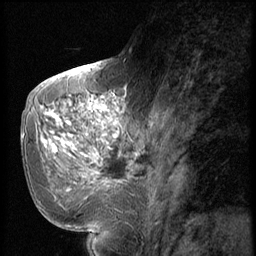
Breast MRI (dynamic contrast-enhanced), one sagittal slice. Slice 26 of 56 in the series (ordered by position). Dynamic contrast-enhanced series, image 2 of 2 at this slice position (ordered by acquisition). 1.5 T. TE 4.2 ms, TR 9 ms. 2.5 mm slice thickness. 256 × 256 image matrix, field of view 180 × 180 mm. Patient: female, 51 years. Case-level facts recorded for this patient, not image findings: setting: breast cancer imaged before/during neoadjuvant chemotherapy; receptor status: triple-negative.
Annotated regions visible in this slice (semi-automatically segmented with operator editing):
- analysis volume of interest (the breast-tissue region the enhancement analysis was run in; not a lesion): bounding box (x1, y1, x2, y2) in pixels: (60, 98, 147, 197)
- tumour enhancement mask (voxels above the 140 % enhancement threshold inside the analysis volume of interest): (62, 98, 125, 157)